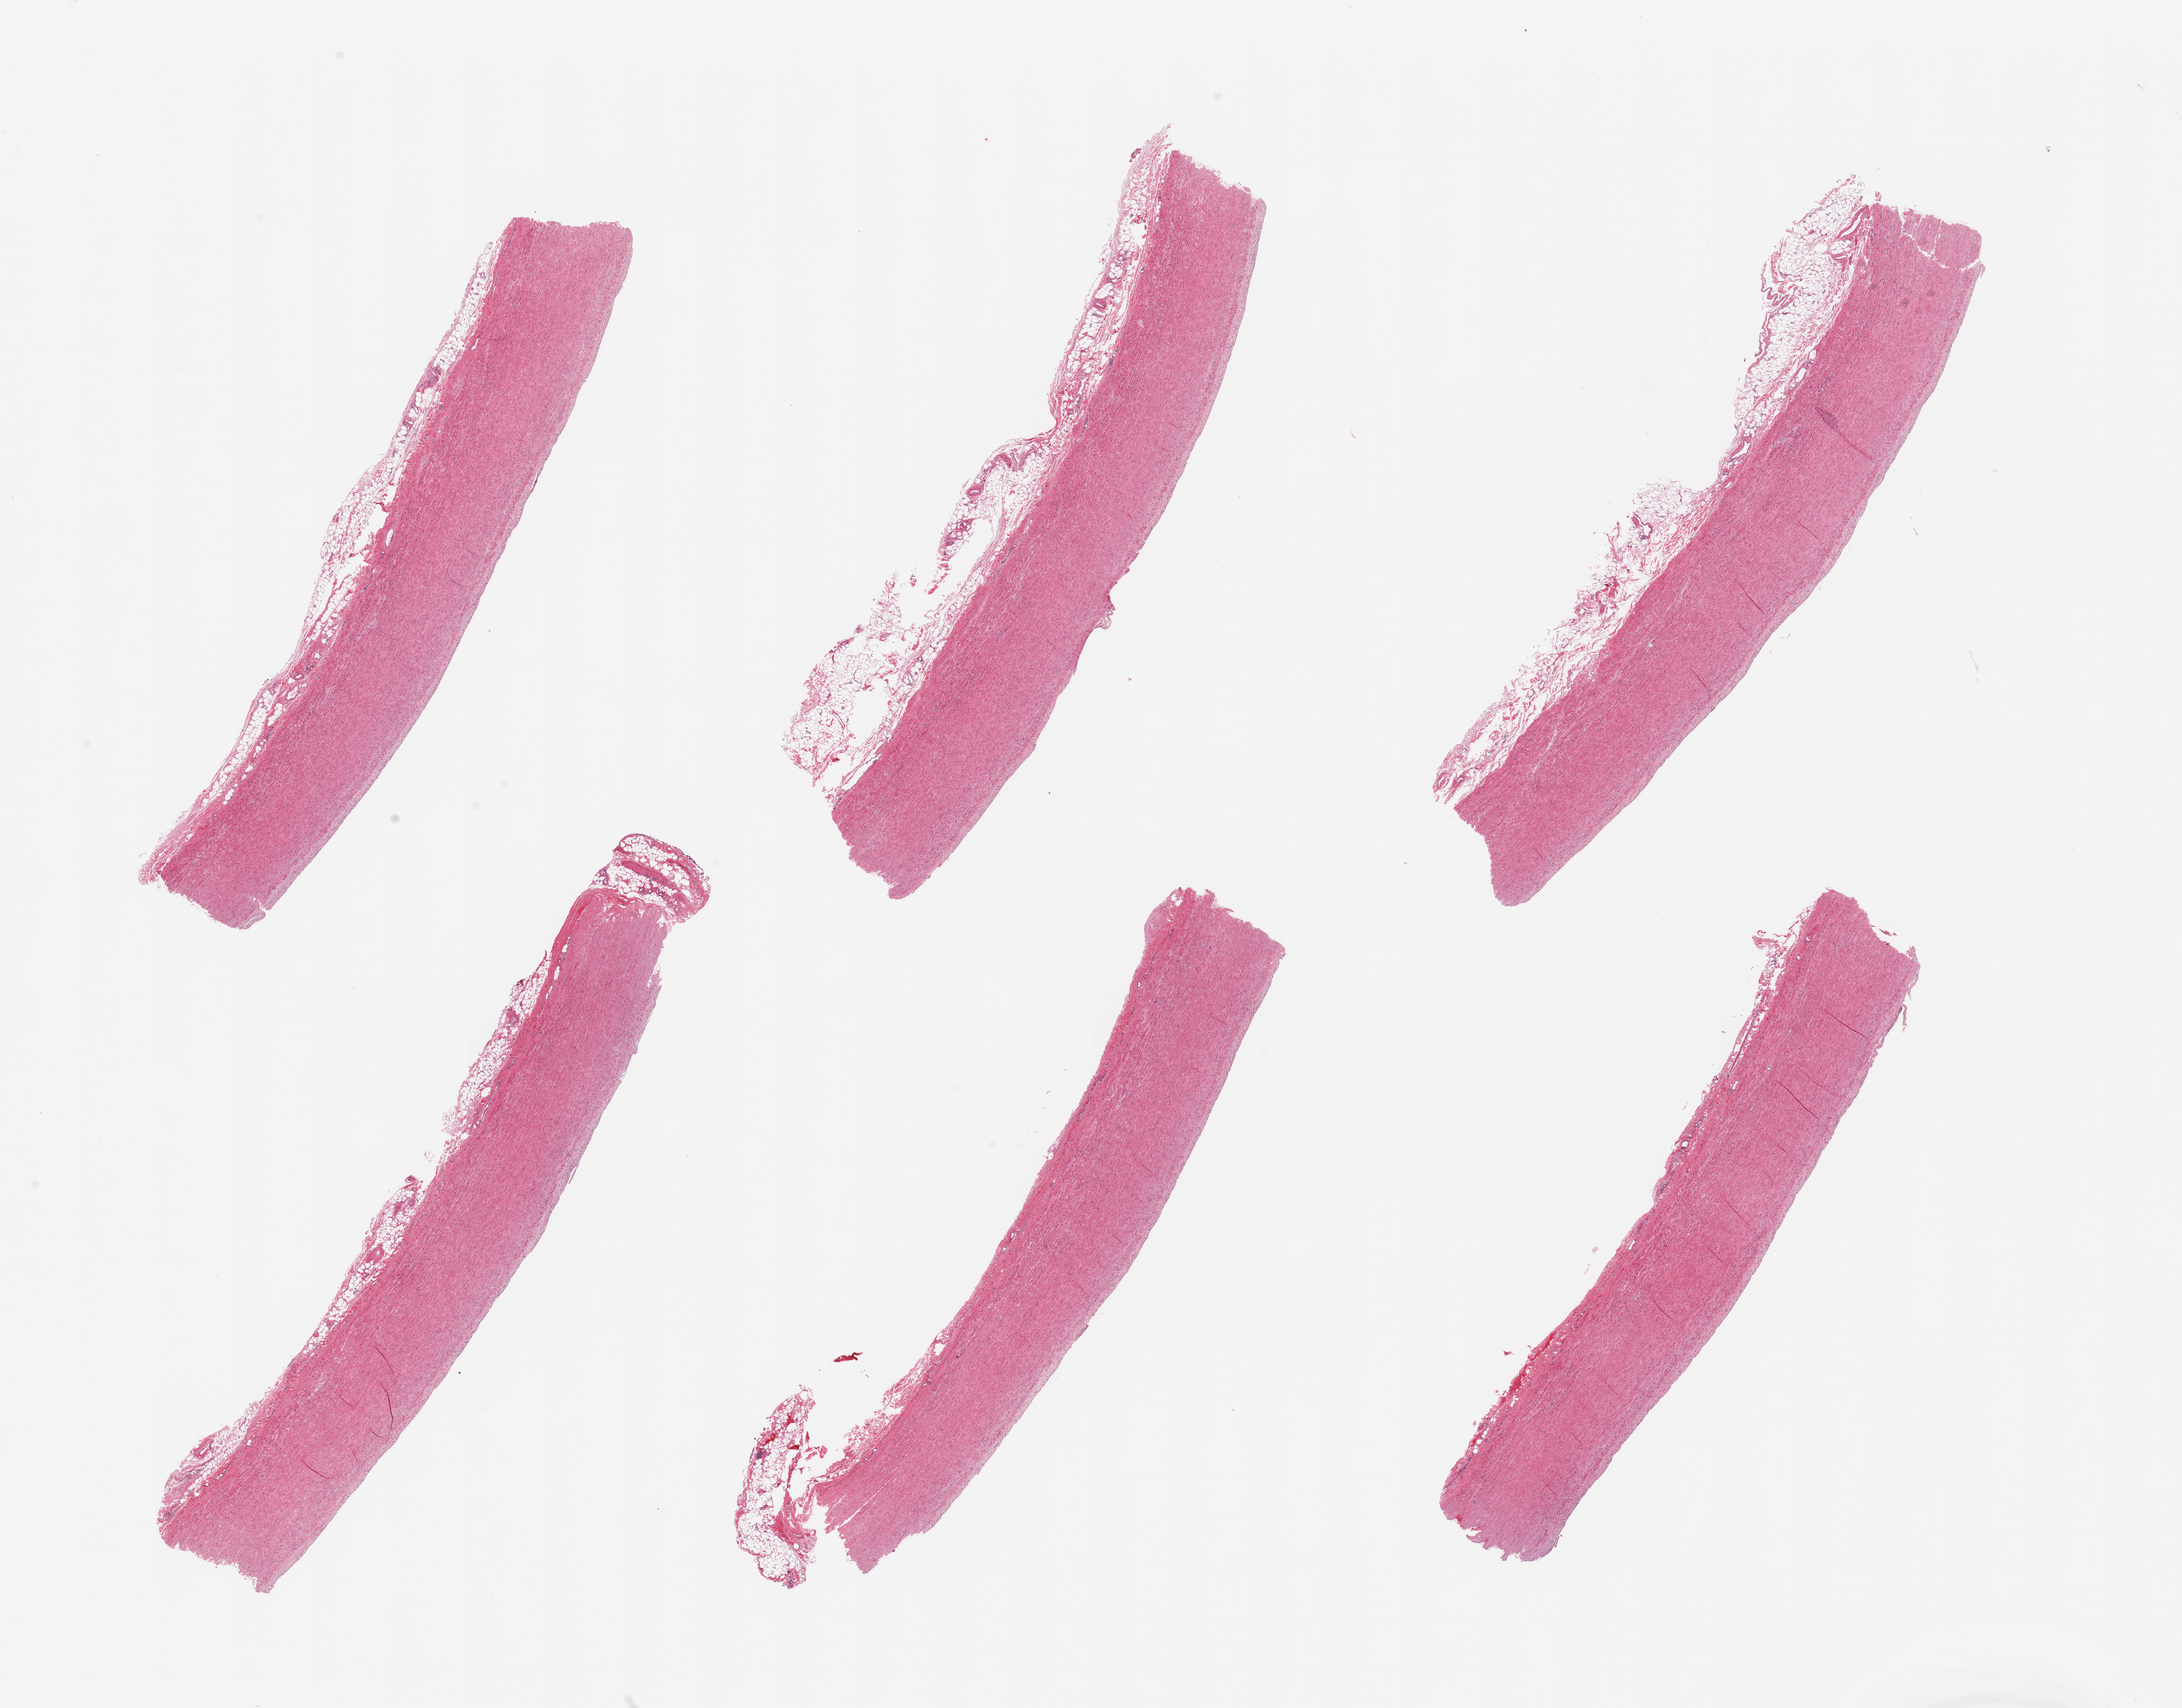
Whole-slide image, H&E stain, brightfield, low-resolution overview of the scanned area, about 27.6 x 21.6 mm, PAXgene-fixed, paraffin-embedded tissue, target tissue: aorta, tissue donor sample. Donor sex: male.
Pathologist's review note for this sample: 6 pieces; some residual attached fat.